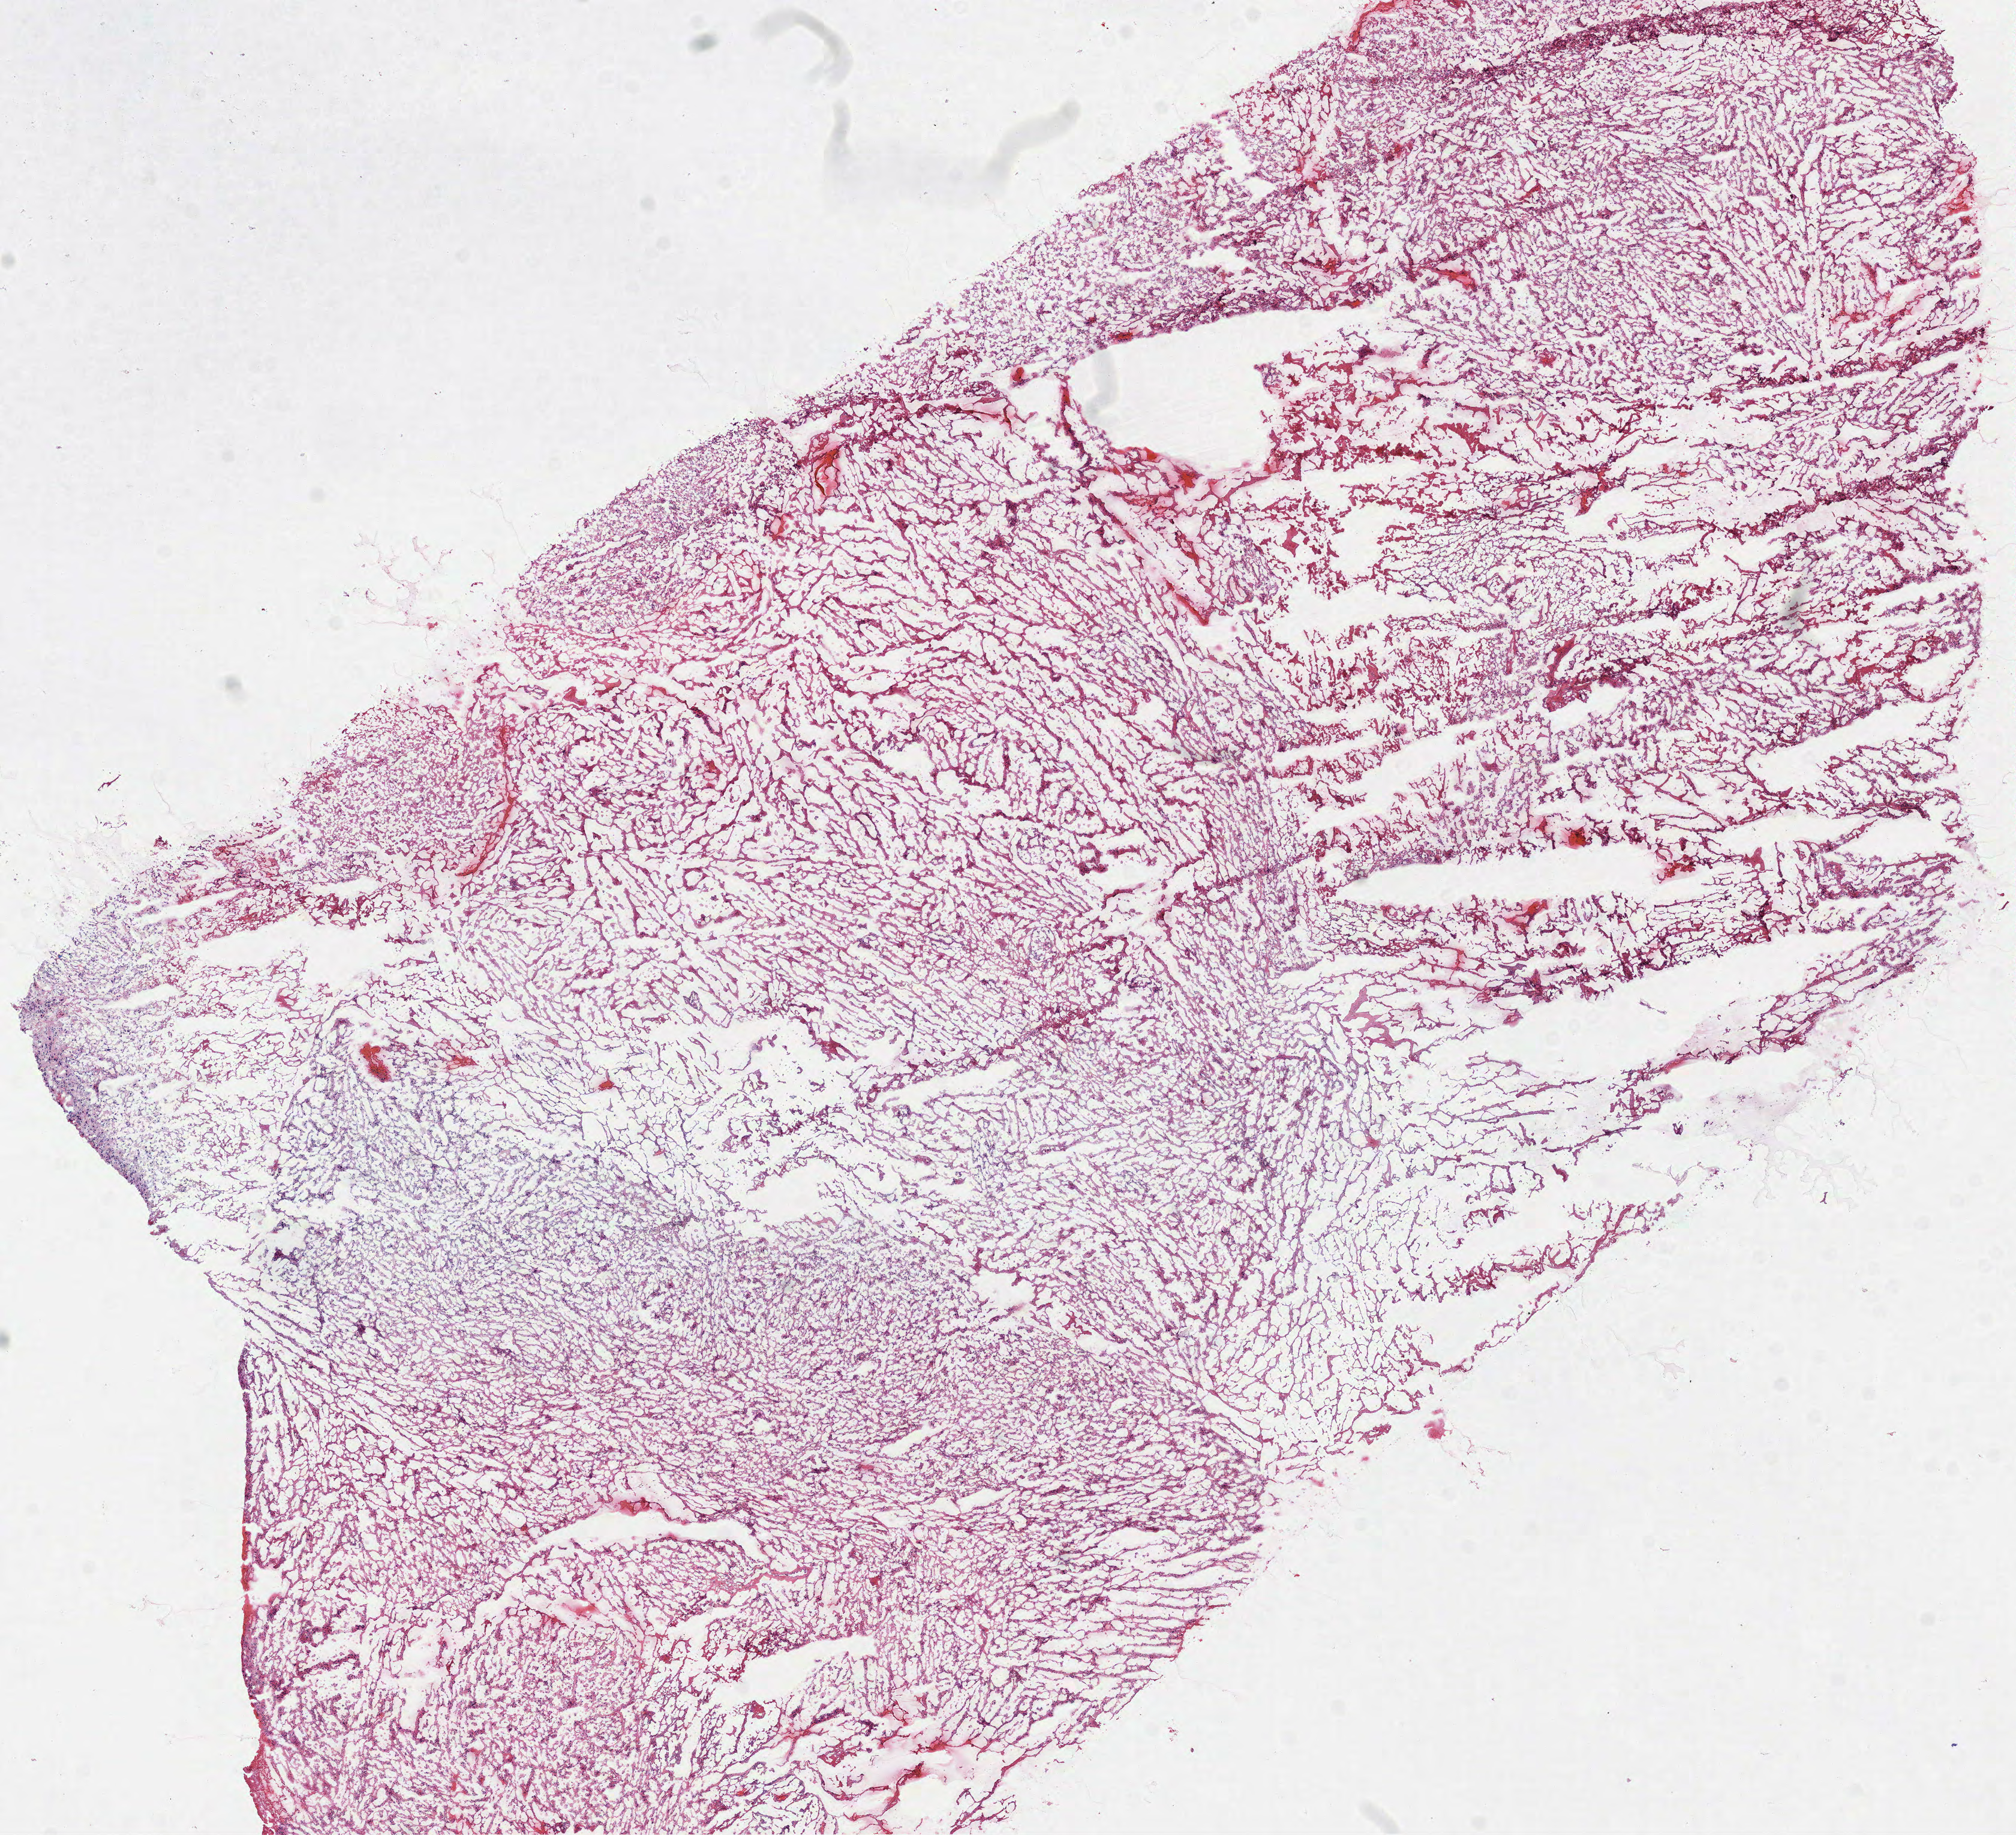
H&E whole-slide image, shown as a low-resolution overview of the whole scanned area (about 13.6 x 12.3 mm), frozen section from the top of the tissue portion, brain, primary tumour sample. Patient: male, age at initial diagnosis 74 years.
Pathologic diagnosis: Glioblastoma.